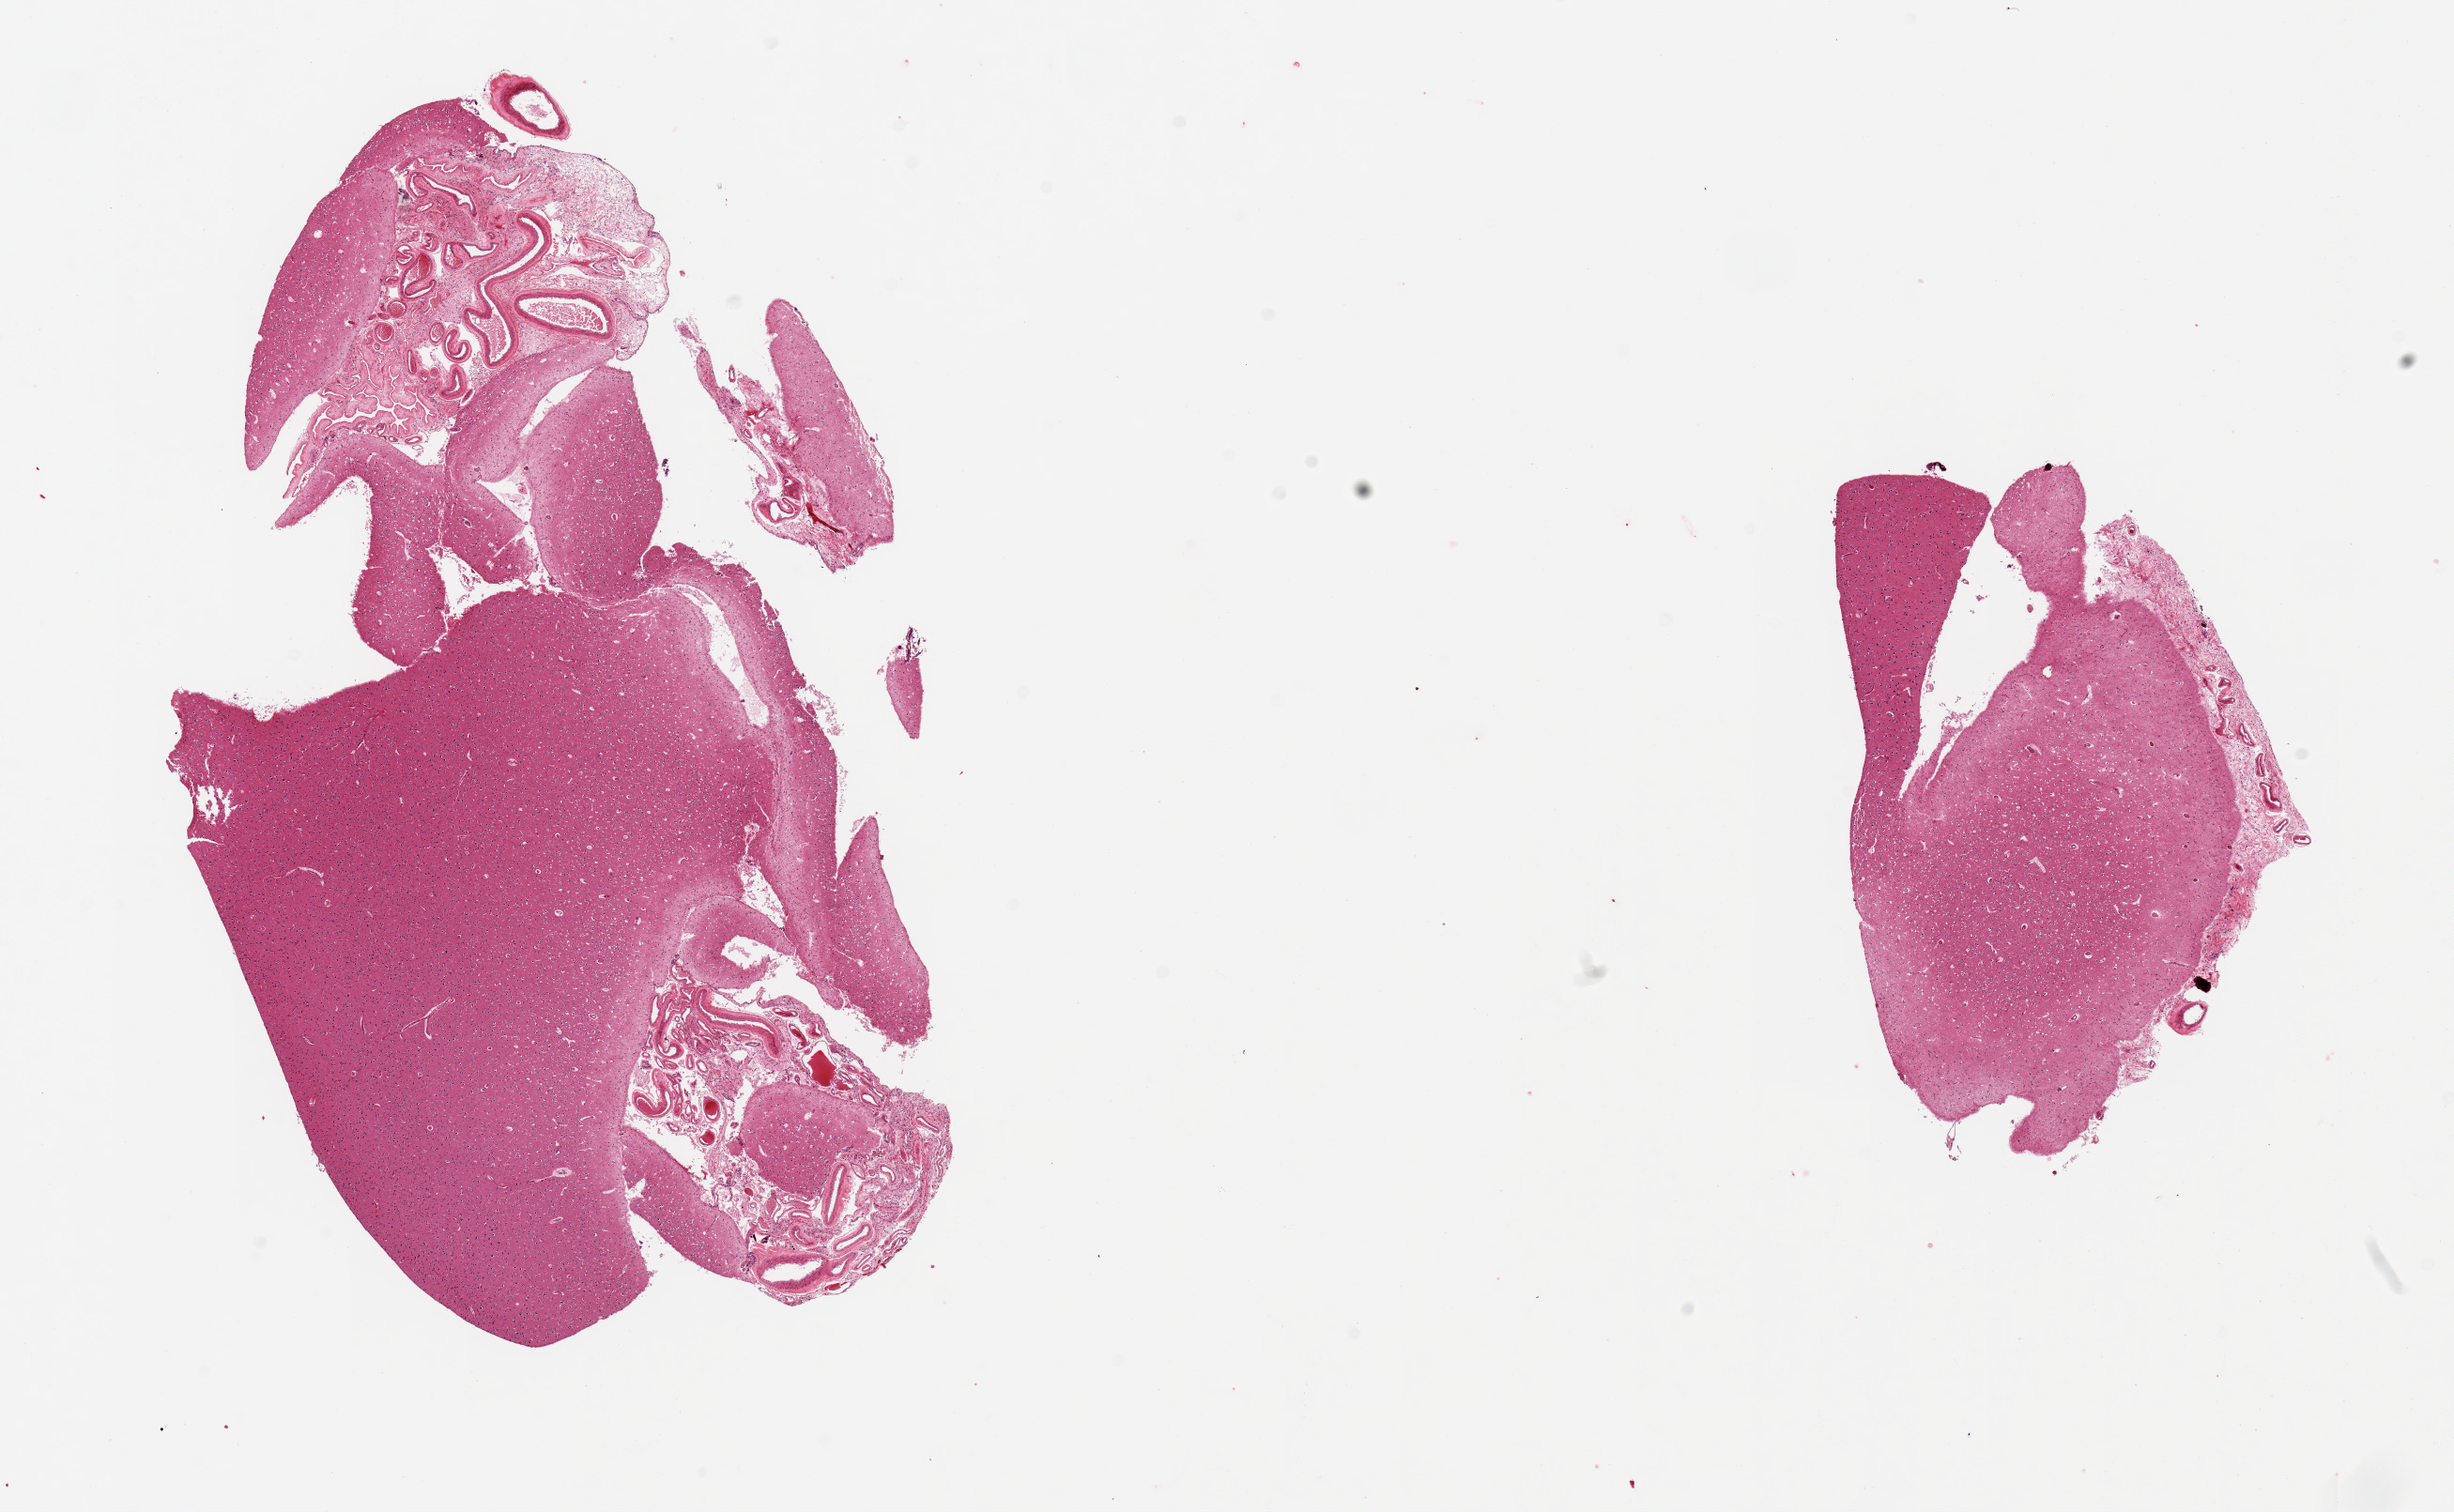
Haematoxylin and eosin whole-slide image, brightfield — shown as a low-resolution overview of the whole scanned area (about 20.7 x 12.7 mm, slide scanned at 20x). PAXgene-fixed, paraffin-embedded tissue. Target tissue: cerebral cortex. Donor tissue sample. Donor sex: female.
Review note (as recorded): 2 pieces; cerebral cortex with attached meninges.